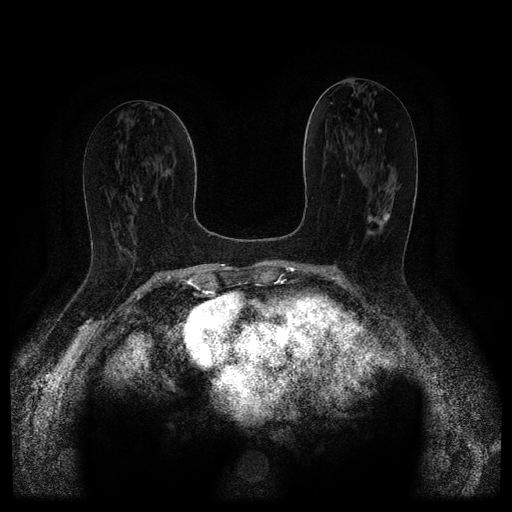
Breast MRI (dynamic contrast-enhanced, multi-phase), one axial slice. Position 52 of 116 along the scan axis. Dynamic contrast-enhanced series, time point 2 of 5 at this slice position (early post-contrast). 1.5 T. TE 2.6 ms, TR 5.4 ms. 2 mm slice thickness. 512 × 512 image matrix. Patient: female, 67 years.
Outlined on this slice (semi-automatic segmentation, software-assisted and operator-edited):
- breast lesion (labelled 'tumour' in the annotation; benign lesions carry a separate 'benign' label): bounding box (x1, y1, x2, y2) in pixels: (367, 213, 390, 234)